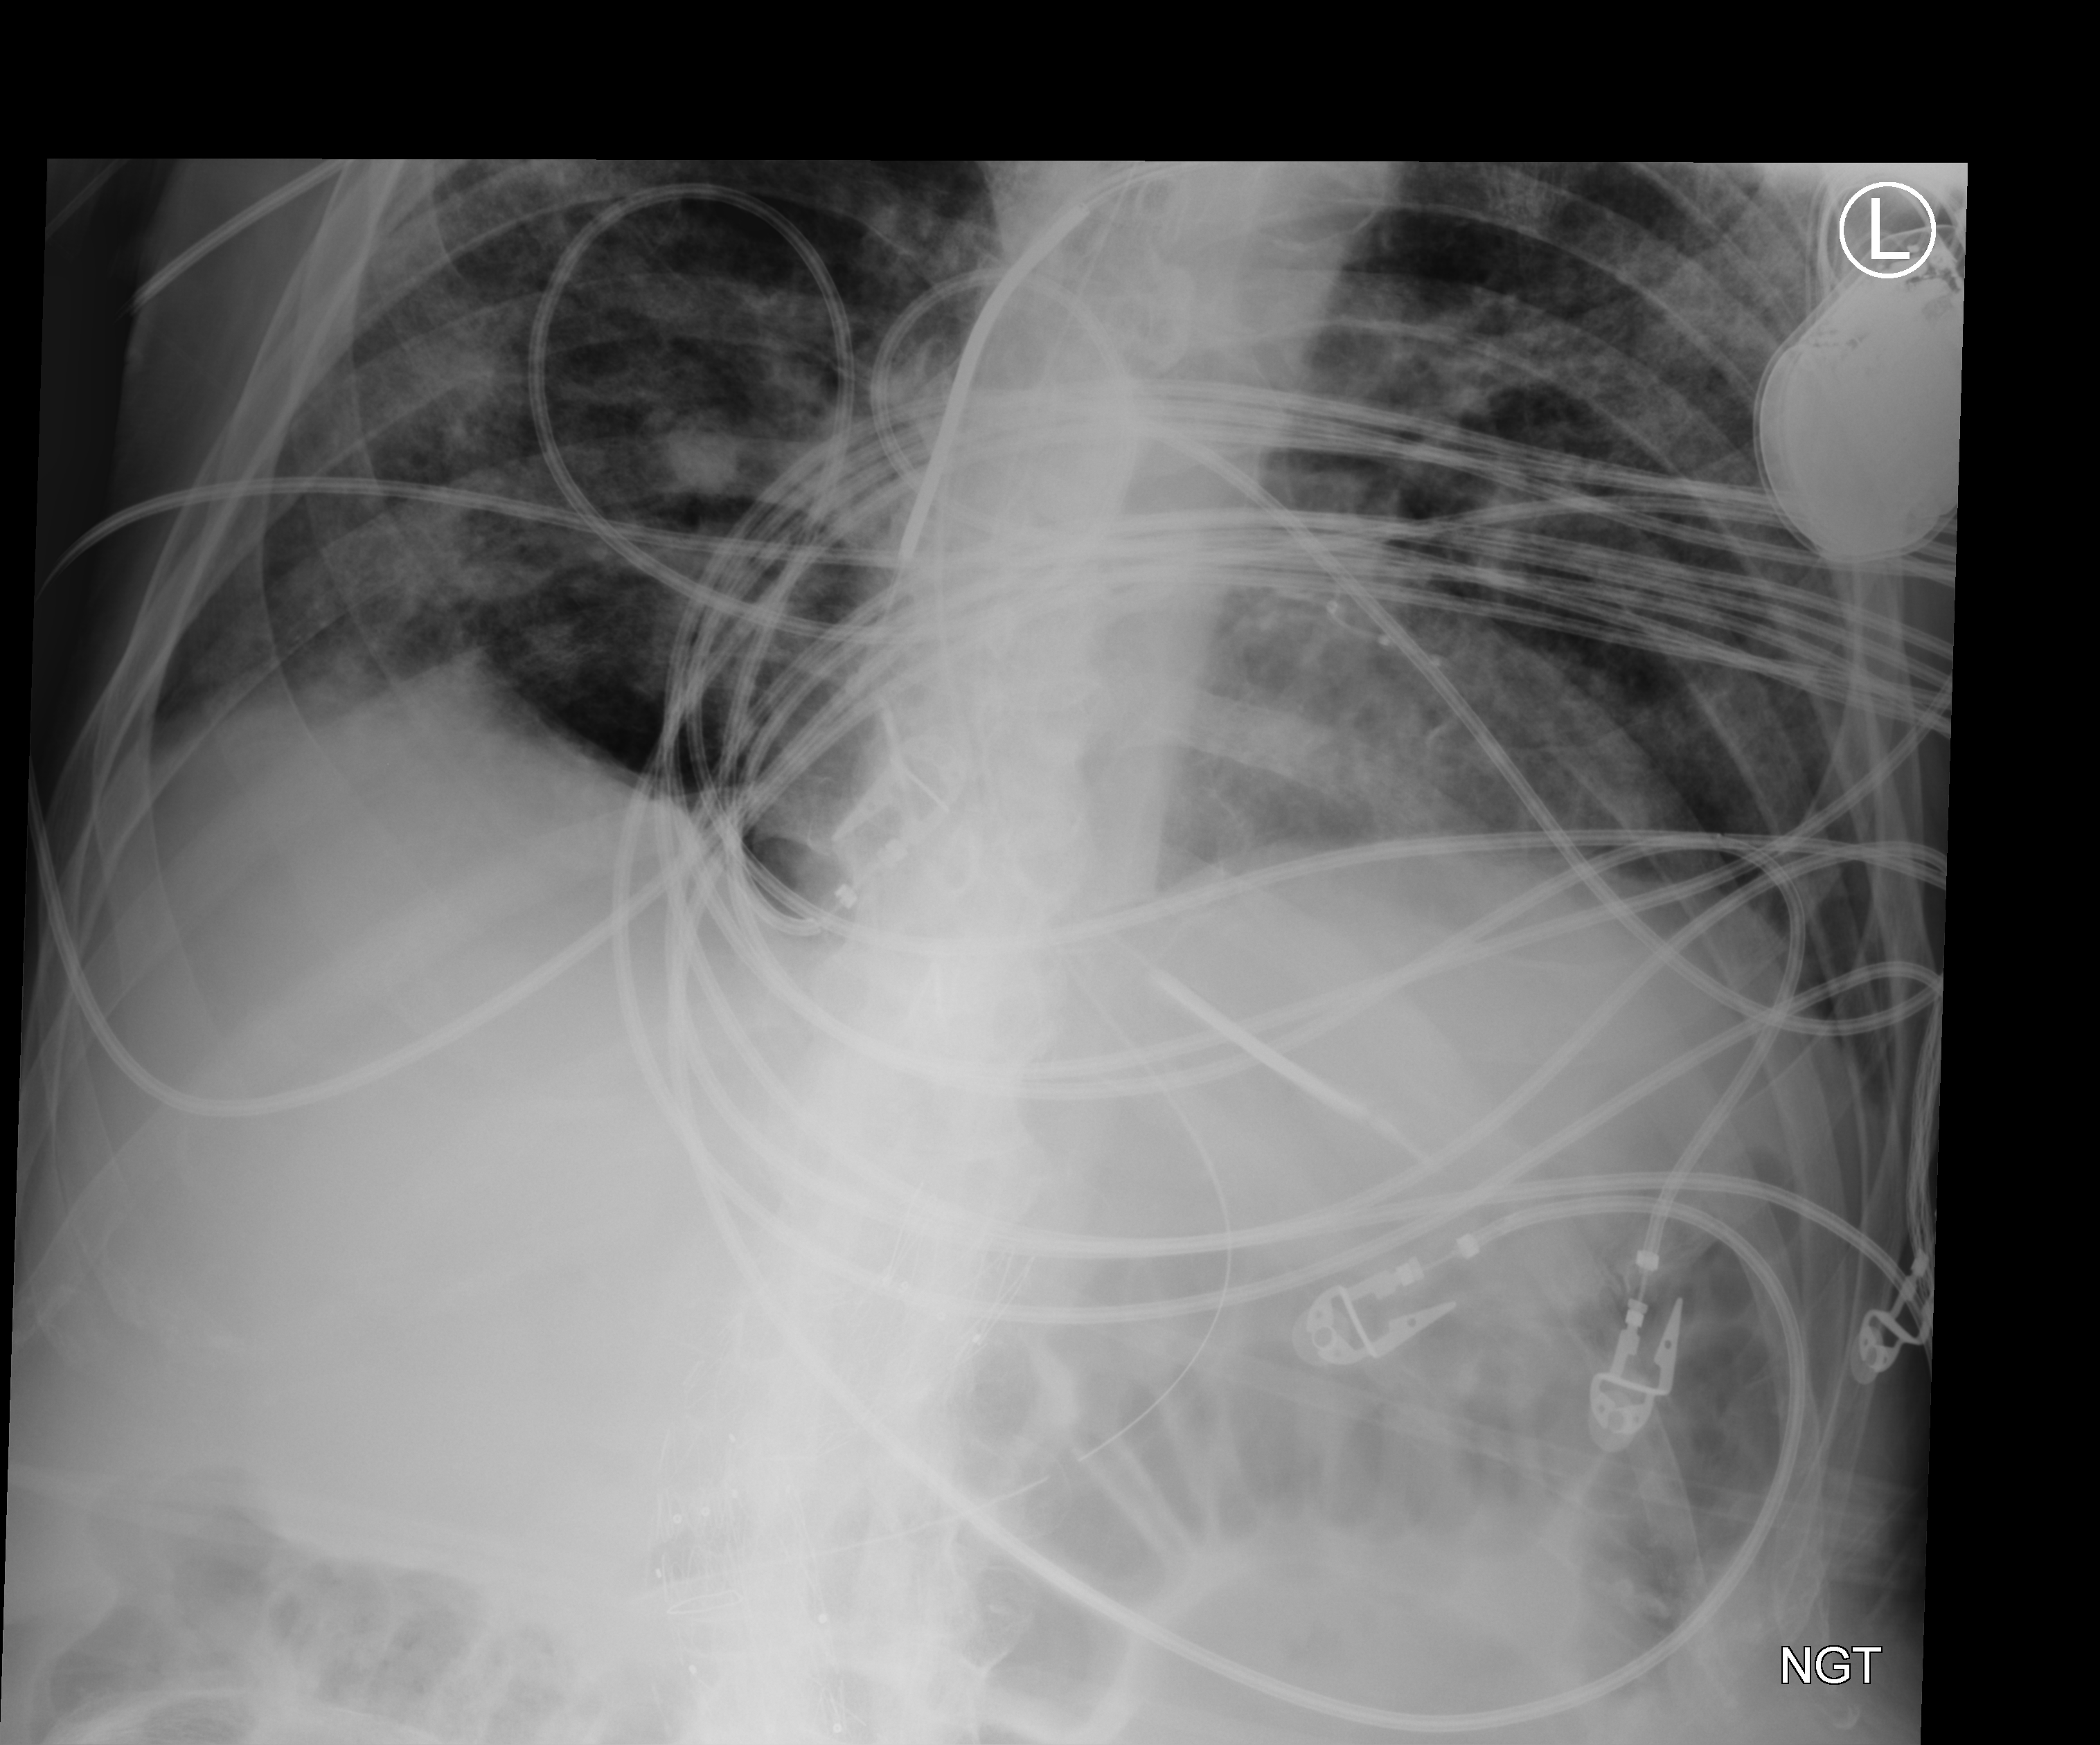
Portable abdomen radiograph; anteroposterior (AP) projection. Patient hospitalised with COVID-19; male, aged 60–74 years.
Admission-level facts for this patient (not findings on this image; timing relative to this image not recorded): smoking status (admission record): former; mechanically ventilated during this hospital stay: yes; other chronic lung disease (admission record): no.